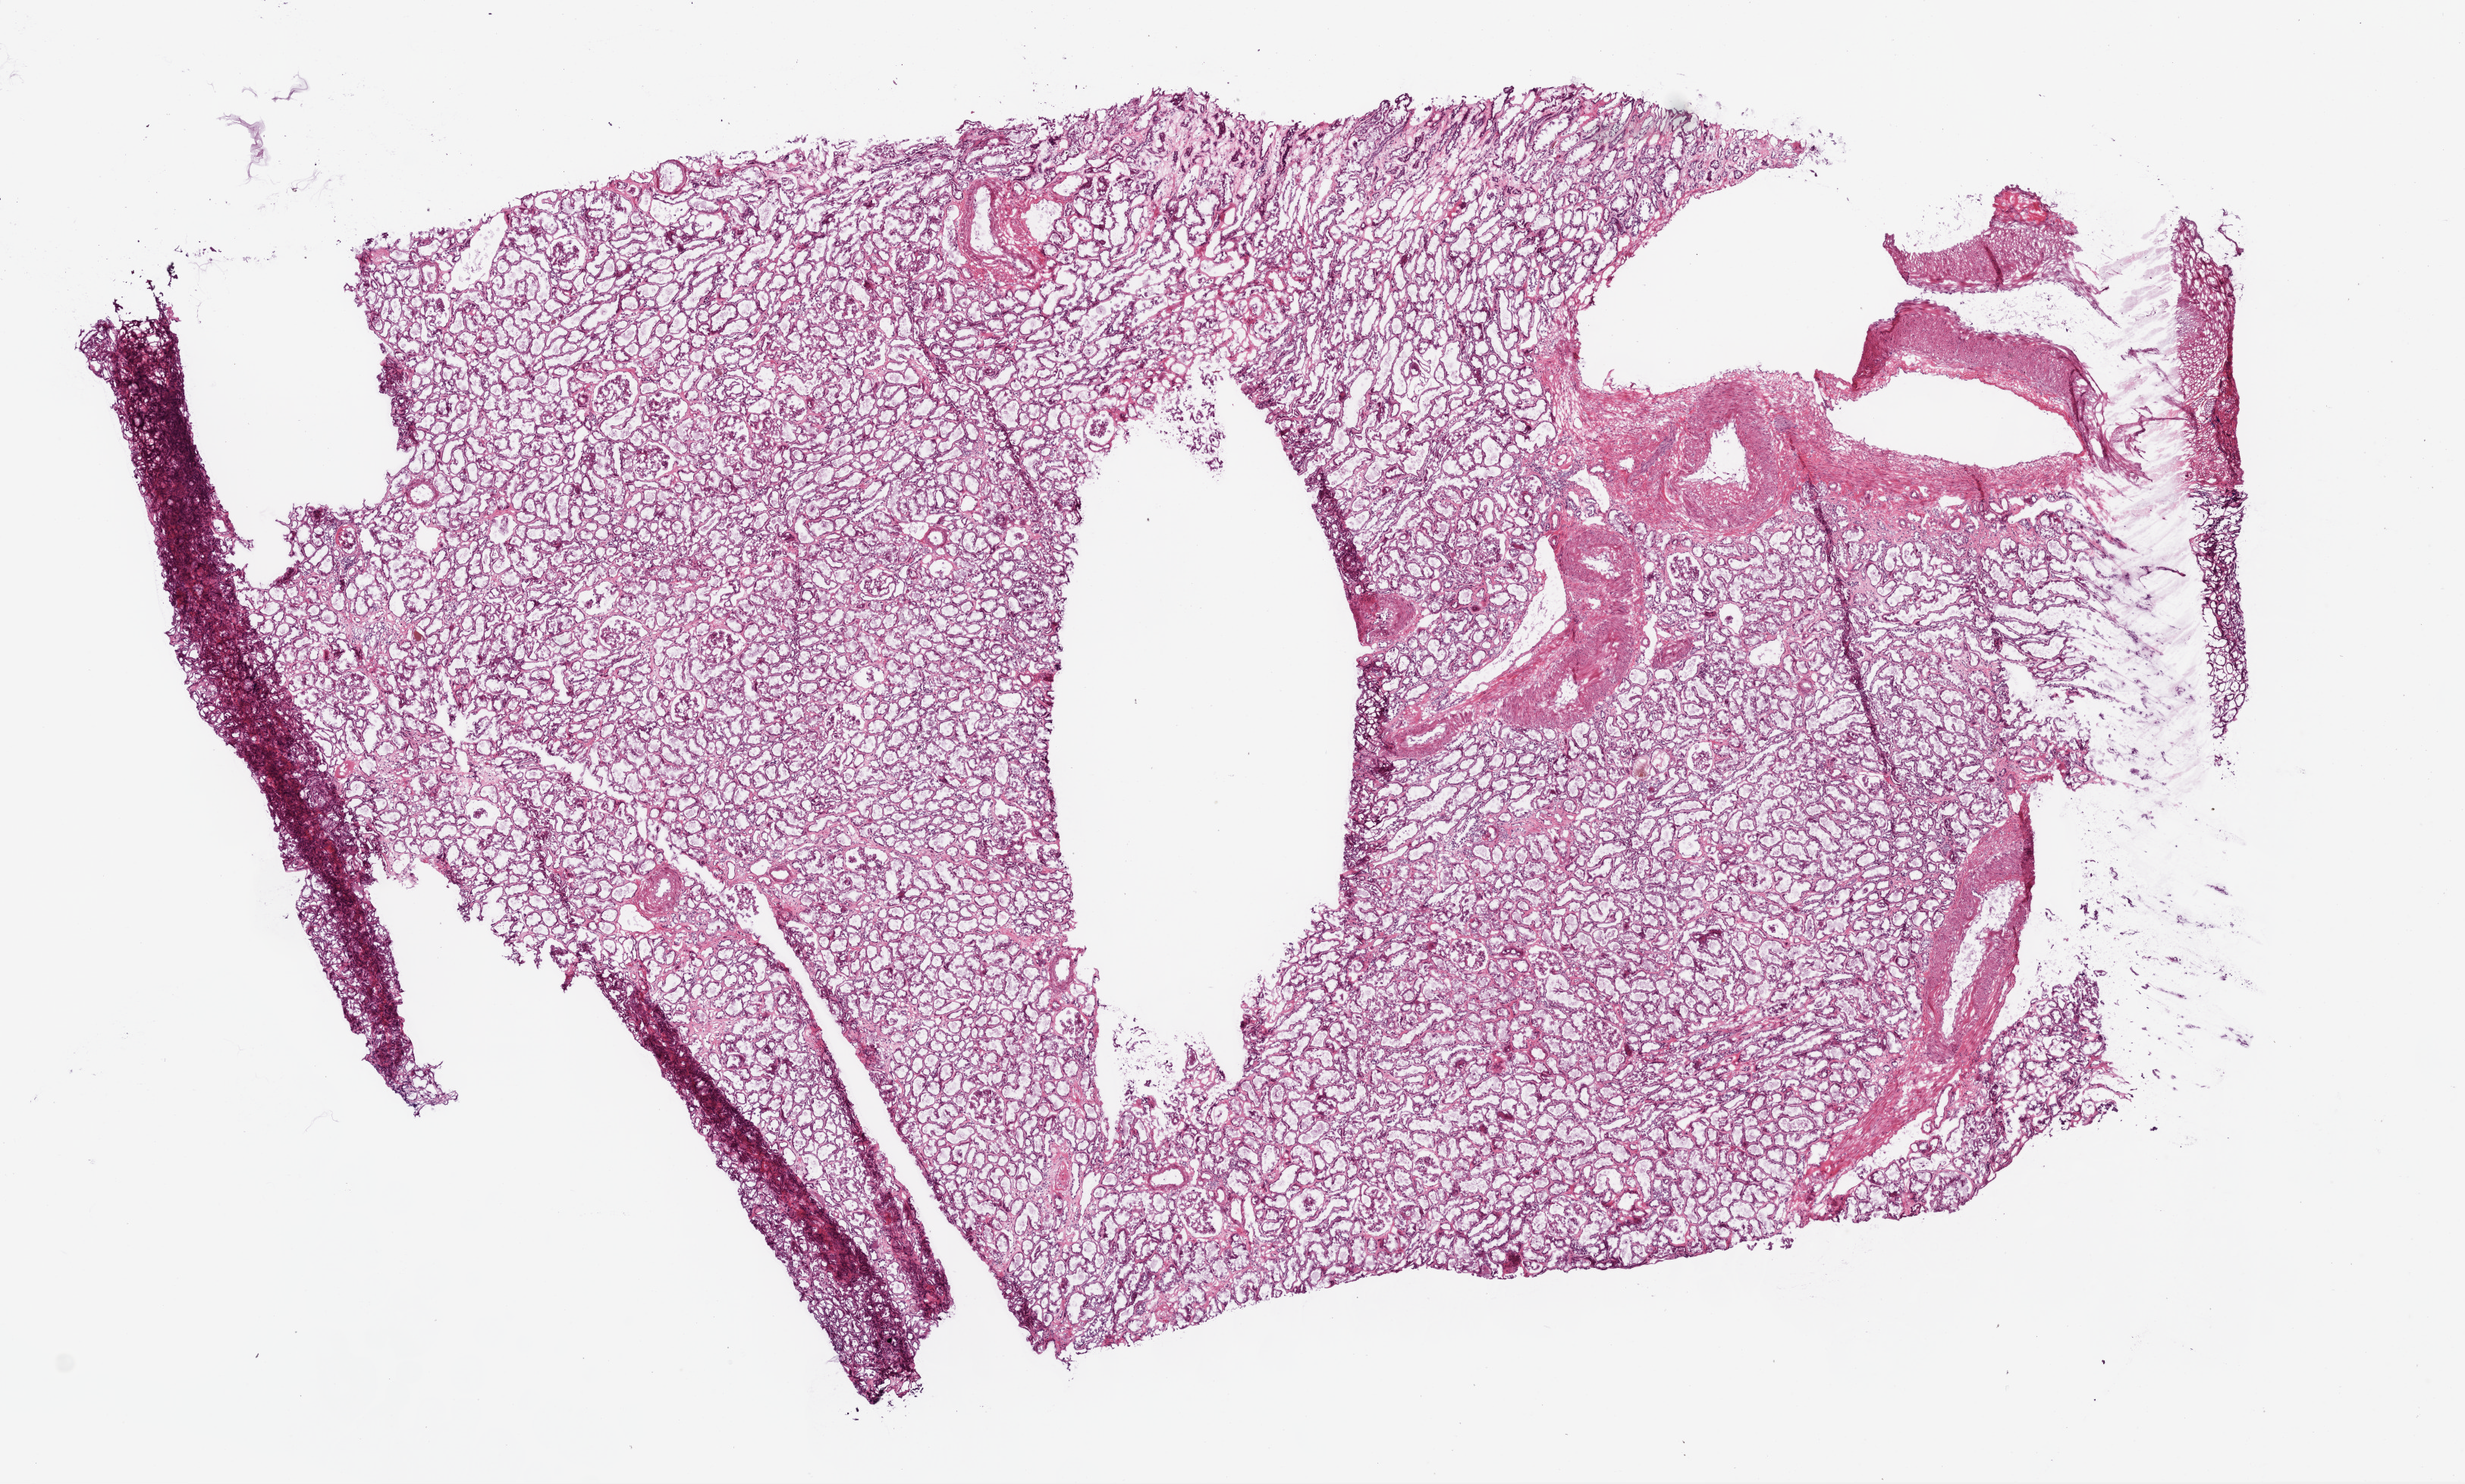
H&E-stained whole-slide image — shown as a low-resolution overview of the whole scanned area (about 13.0 x 7.9 mm, slide scanned at 20x), frozen section, sample: solid tissue normal (non-tumour tissue), kidney. Patient: male, age at initial diagnosis 74 years.
This section: solid tissue normal (non-tumour) sample from the same patient. Patient diagnosis: Clear cell adenocarcinoma, NOS.